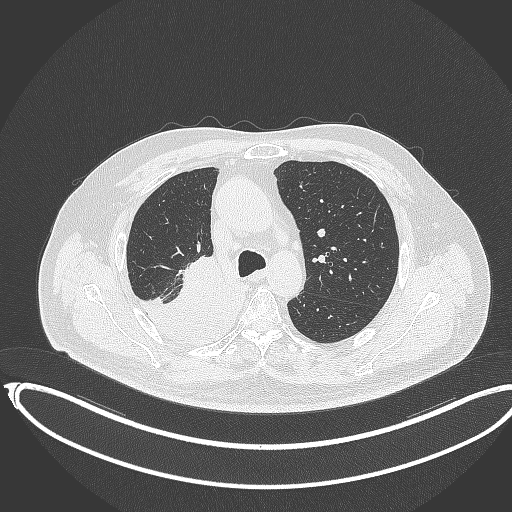
Chest CT, one axial slice. Slice 249 of 403 in the series (ordered by position). 120 kVp. Lung window (W 1500 / L -600 HU). 1 mm slice thickness. 512 × 512 image matrix, field of view 436 × 436 mm. Patient: male, 68 years. Case-level facts recorded for this patient, not image findings: clinical TNM (as recorded): T2a N0 M0.
Structures marked on this image (rectangle marked by the reading radiologist):
- lung tumour (recorded histology: adenocarcinoma): bounding box <129,254,244,349> (left, top, right, bottom; pixels)